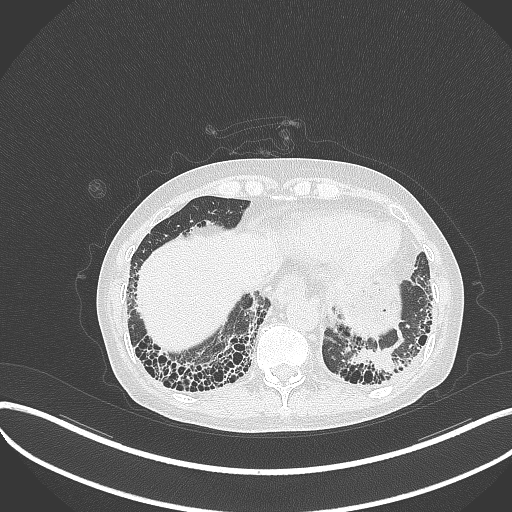
Chest CT, one axial slice. Slice 61 of 373 in the series (ordered by position). Reconstruction kernel B70f. 120 kVp. Lung window (W 1500 / L -600 HU). 1 mm slice thickness. 512 × 512 image matrix. Patient: female, 56 years. From the clinical record (not read from this slice): clinical TNM (as recorded): T1 N0 M0.
Structures marked on this image (bounding box drawn by a radiologist):
- lung tumour (recorded histology: adenocarcinoma): bounding box [x1, y1, x2, y2] px = [349, 346, 396, 377]